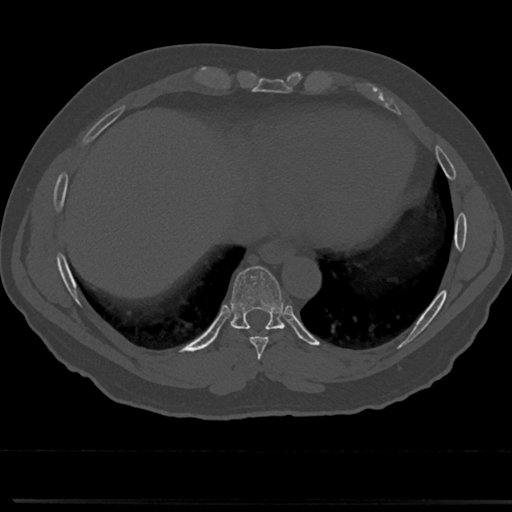
CT including the spine, one axial slice; position 325 of 817 along the scan axis; reconstruction kernel Br40s/3; bone window (W 1800 / L 400 HU); 512 × 512 image matrix, field of view 355 × 355 mm. Male patient, age 61 years. From the clinical record (not read from this slice): primary cancer: prostate.
Outlined on this slice (semi-automatic segmentation, software-assisted and operator-edited):
- T7 vertebra: bounding box (x1, y1, x2, y2) in pixels: (258, 354, 266, 376)
- T8 vertebra: (212, 270, 310, 357)